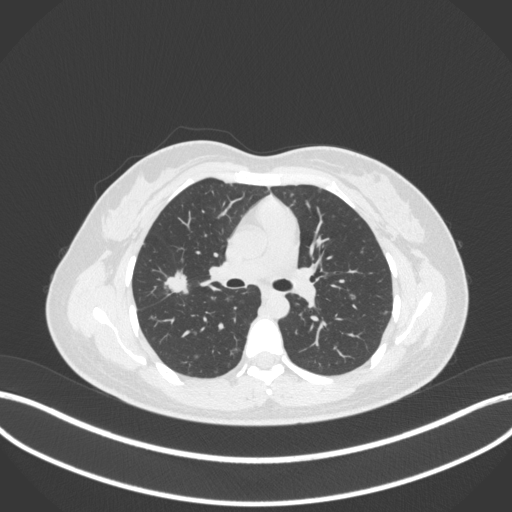
Chest CT, one axial slice. Position 201 of 214 along the scan axis. Reconstruction kernel B31f. Lung window (W 1500 / L -600 HU). 512 × 512 image matrix. Female patient, age 33 years. From the clinical record (not read from this slice): clinical TNM (as recorded): T1c N0 M0.
Annotated regions visible in this slice (bounding box drawn by a radiologist):
- lung tumour (recorded histology: adenocarcinoma): bounding box (x1, y1, x2, y2) in pixels: (161, 263, 192, 300)